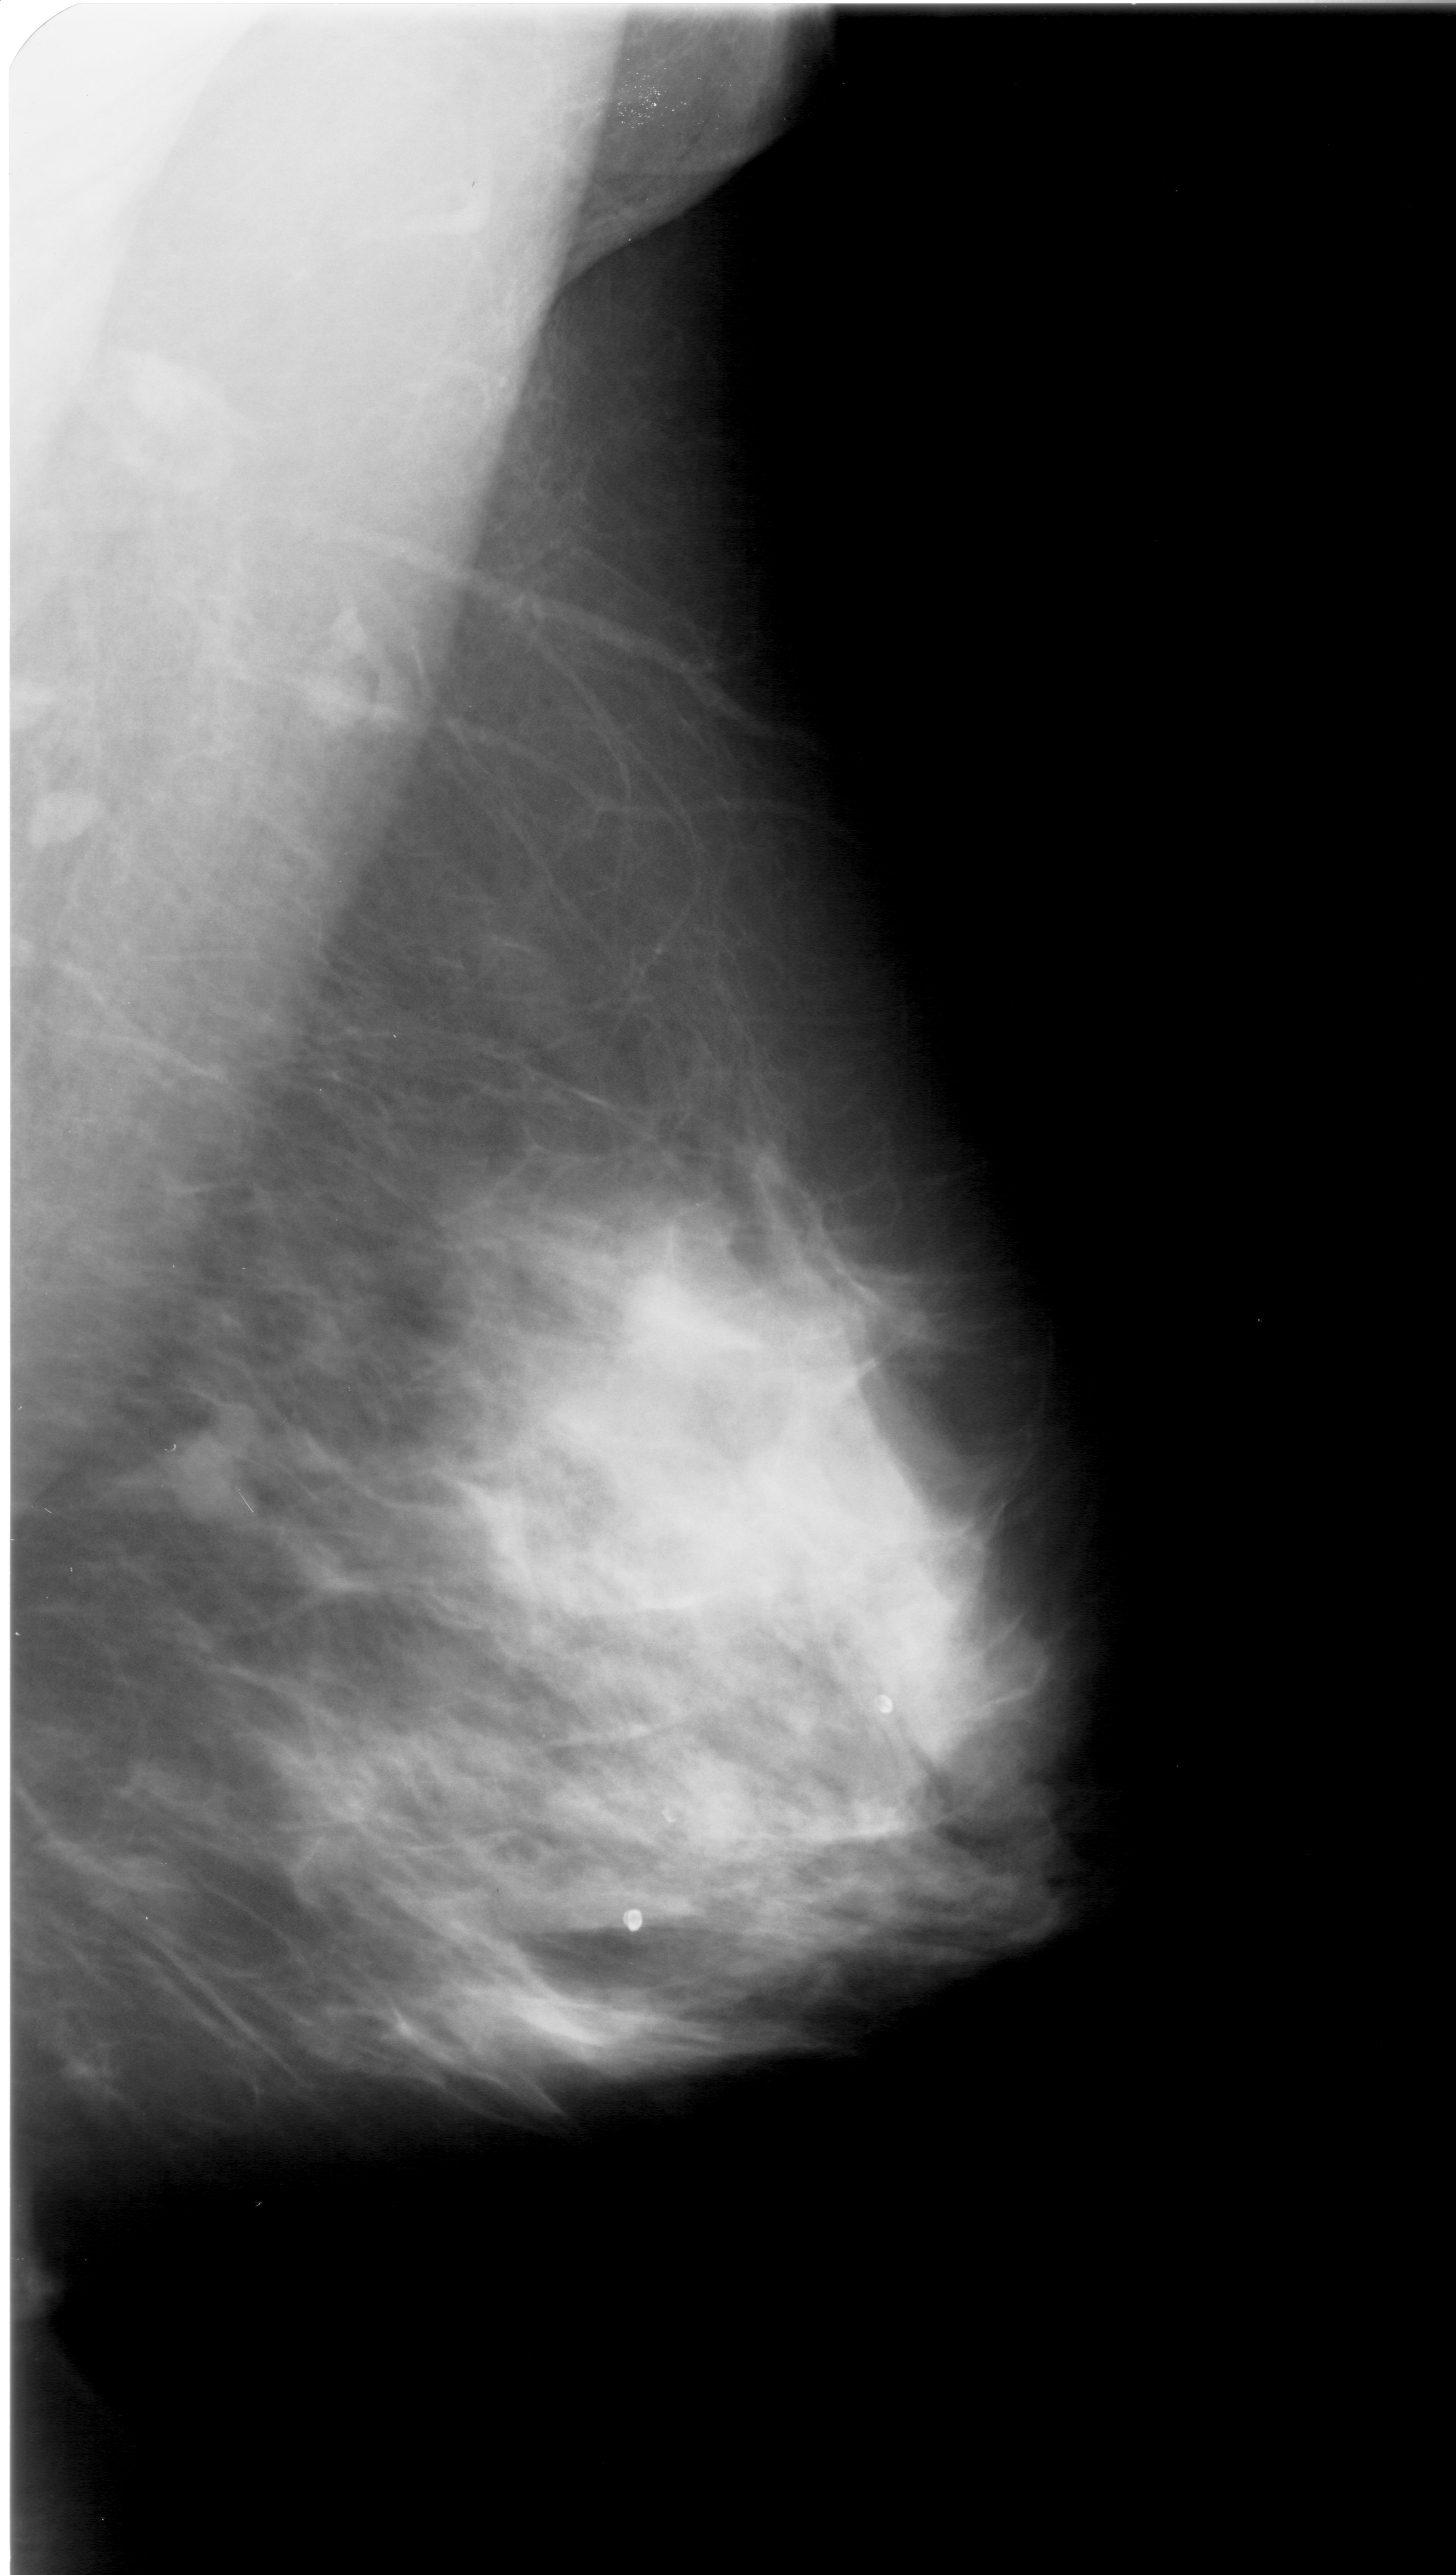
Digitized screen-film mammogram; right breast; mediolateral oblique (MLO) view; BI-RADS breast density category 4 (scale 1–4).
Mass, shape lobulated, margins ill defined; BI-RADS assessment category 4; subtlety rating 2 on a 1 (subtle) to 5 (obvious) scale; pathology (as recorded): malignant.